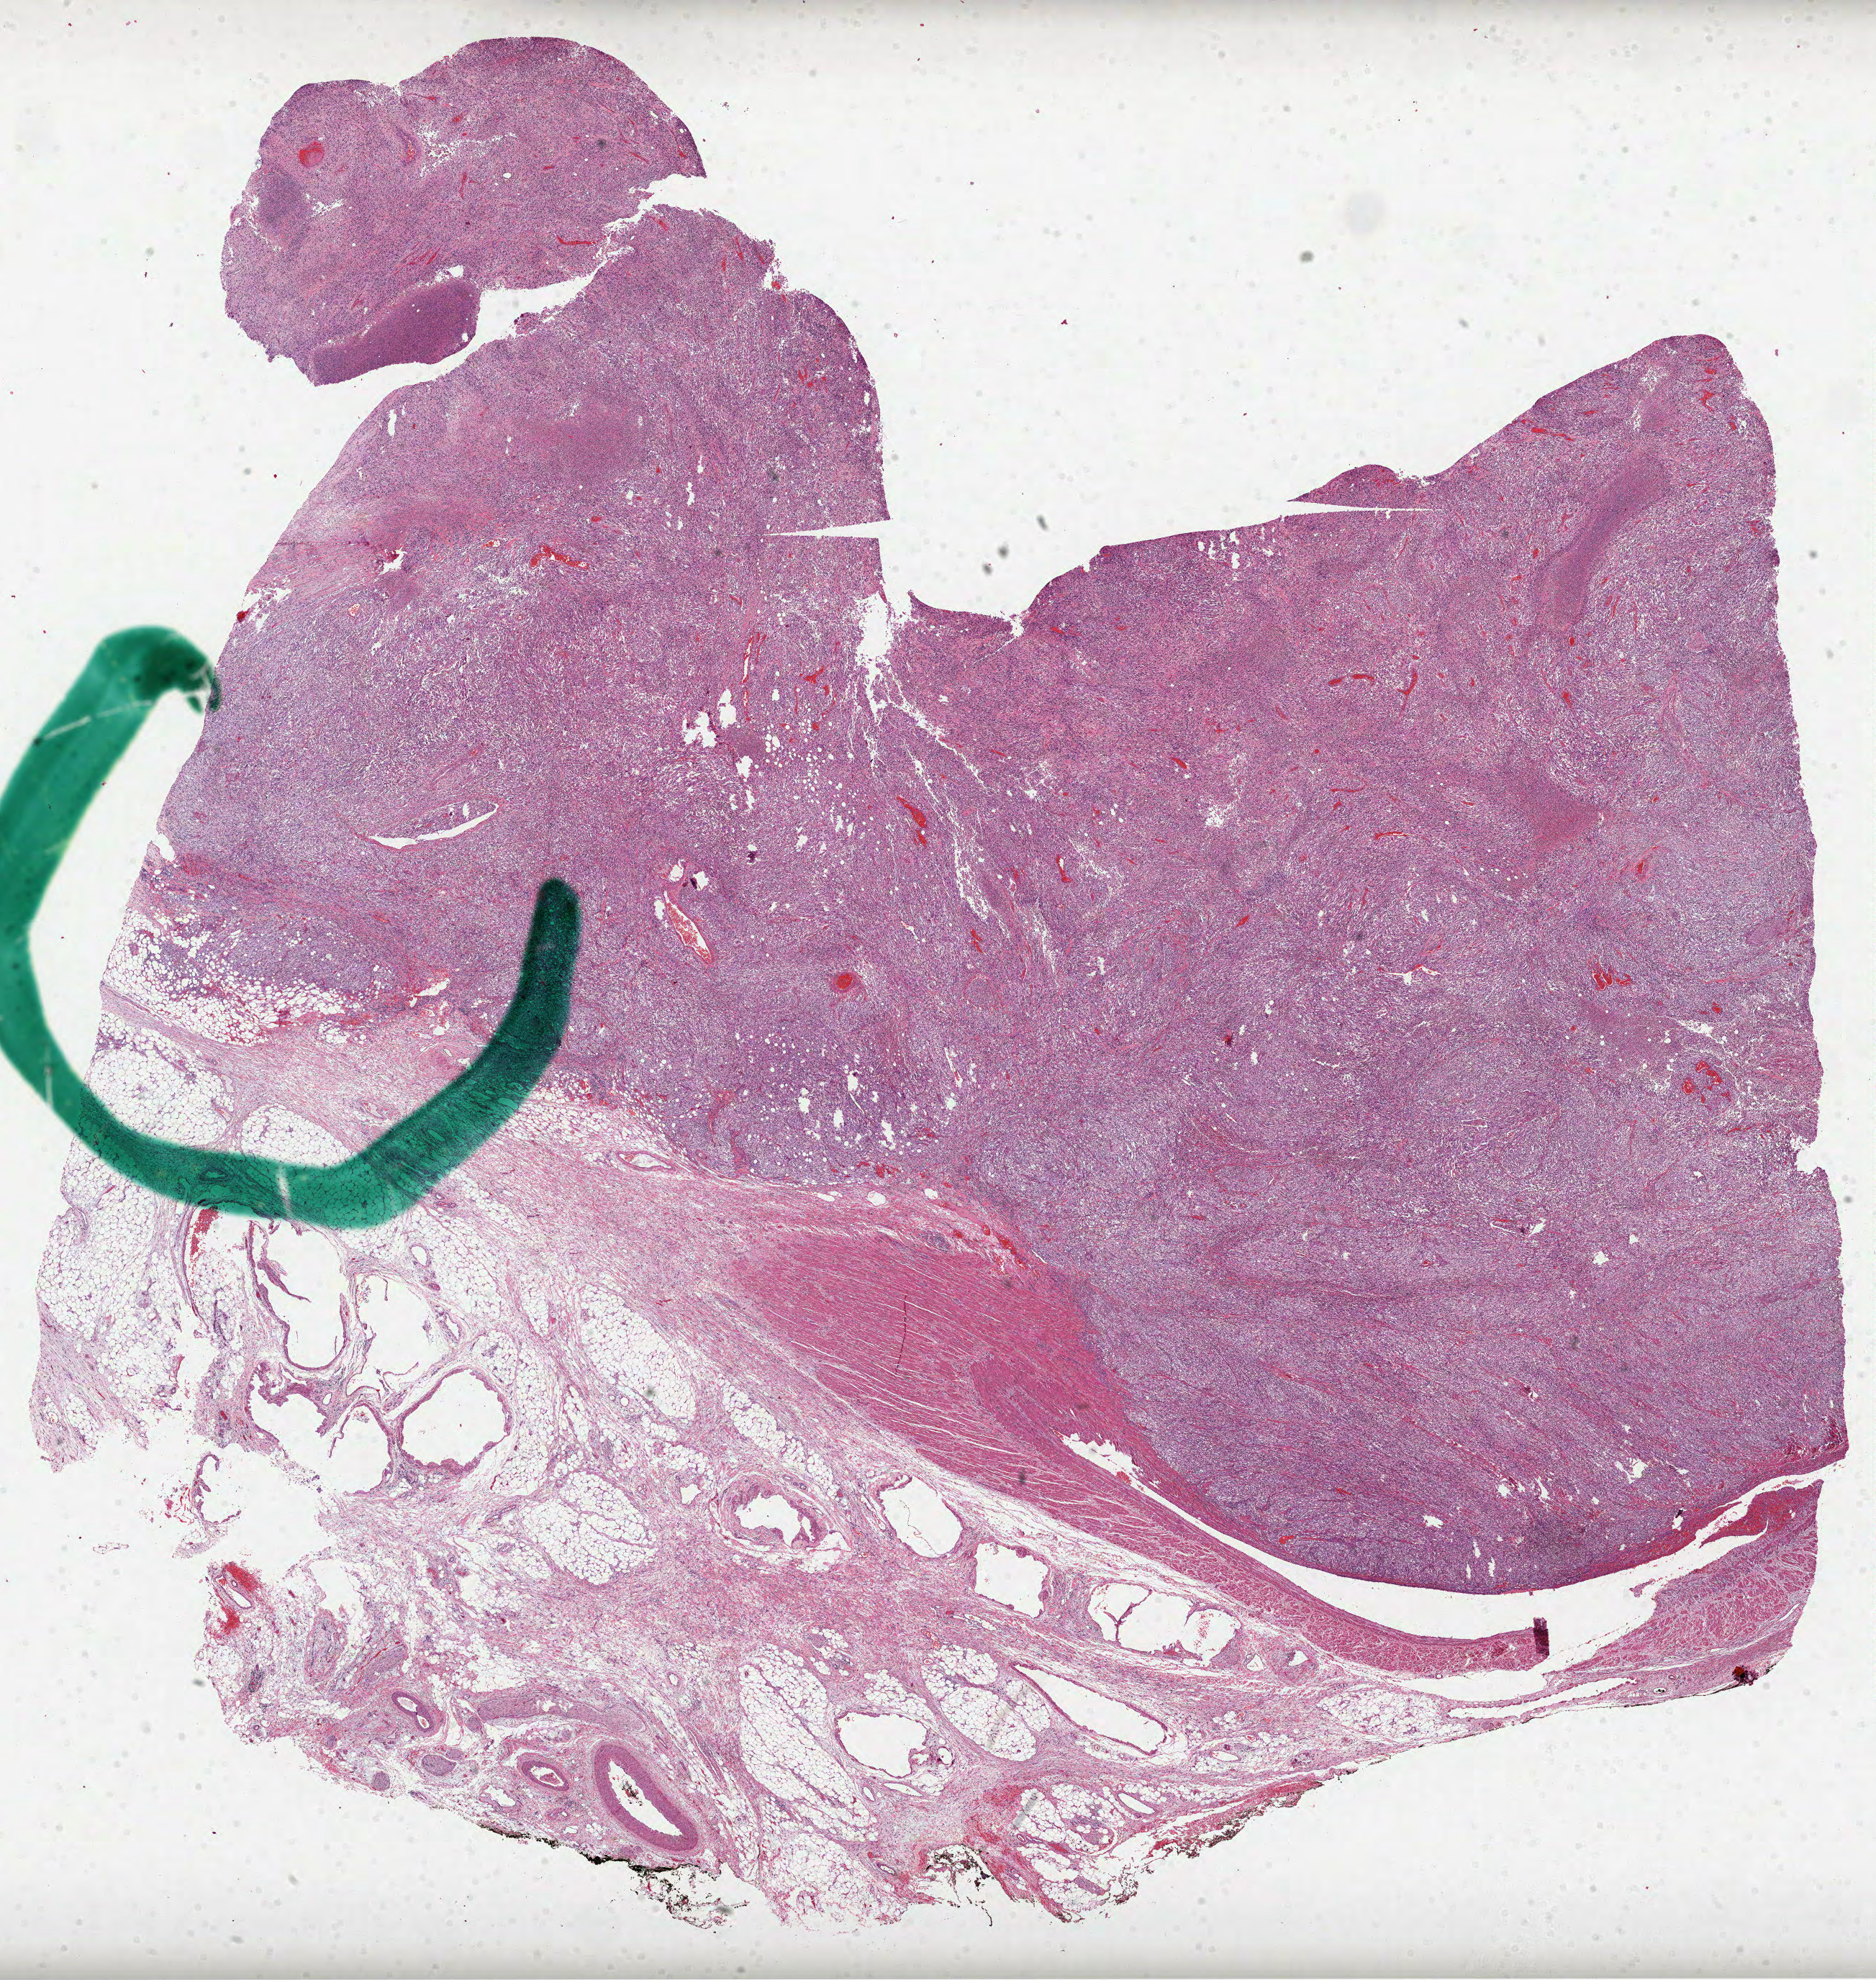
H&E-stained whole-slide image, whole scanned area (about 21.0 x 22.2 mm, from a 40x scan) shown as a low-resolution overview, formalin-fixed paraffin-embedded (FFPE) diagnostic section, kidney, primary tumour sample. Female patient; age at initial diagnosis 72 years. Histologic grade: G4 (undifferentiated).
AJCC pathologic stage: III. Diagnosis: Clear cell adenocarcinoma, NOS. Laterality: left.